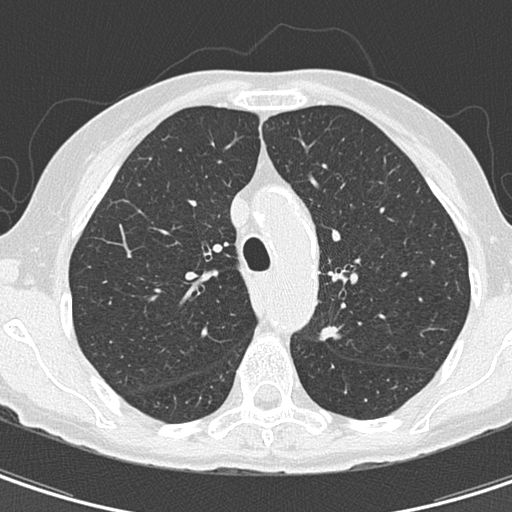
Axial slice from a low-dose chest CT screening exam; baseline screening round; lung window (W 1500 / L -600 HU); 2 mm slice thickness; lung (sharp) reconstruction kernel (B50f); 512 × 512 image matrix, field of view 260 × 260 mm. Female participant, aged 67 years at enrolment. Current smoker at enrolment.
• Expert reader's lesion annotation, bounding box <298,313,358,360> (left, top, right, bottom; pixels).
• The exam's reader record, not a measurement of the box and not confirmed to be the same lesion: non-calcified nodule or mass ≥4 mm, left upper lobe, 11 × 8 mm, spiculated (stellate) margins, soft tissue attenuation.
• Lung cancer was diagnosed 73 days after this screen: adenocarcinoma, NOS, left upper lobe, poorly differentiated (G3), stage IA (AJCC 6th edition), 13 mm at pathology.